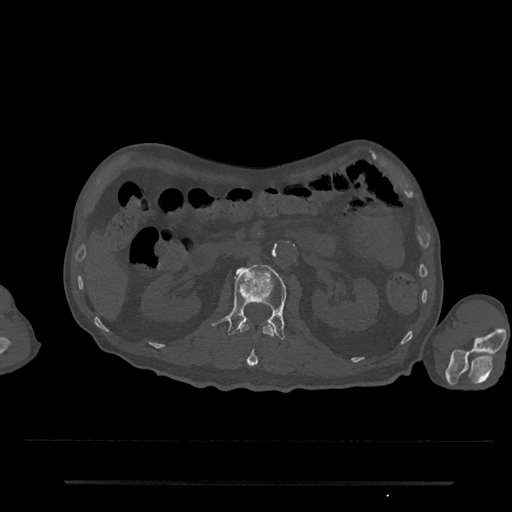
CT including the spine, one axial slice; slice 84 of 797 in the series (ordered by position); 120 kVp; bone window (W 1800 / L 400 HU); 512 × 512 image matrix, field of view 427 × 427 mm. Male patient, age 74 years. From the clinical record (not read from this slice): primary cancer: prostate.
Structures marked on this image (semi-automatic segmentation, software-assisted and operator-edited):
- L1 vertebra: bounding box (x1, y1, x2, y2) in pixels: (239, 322, 274, 367)
- L2 vertebra: (212, 264, 287, 340)